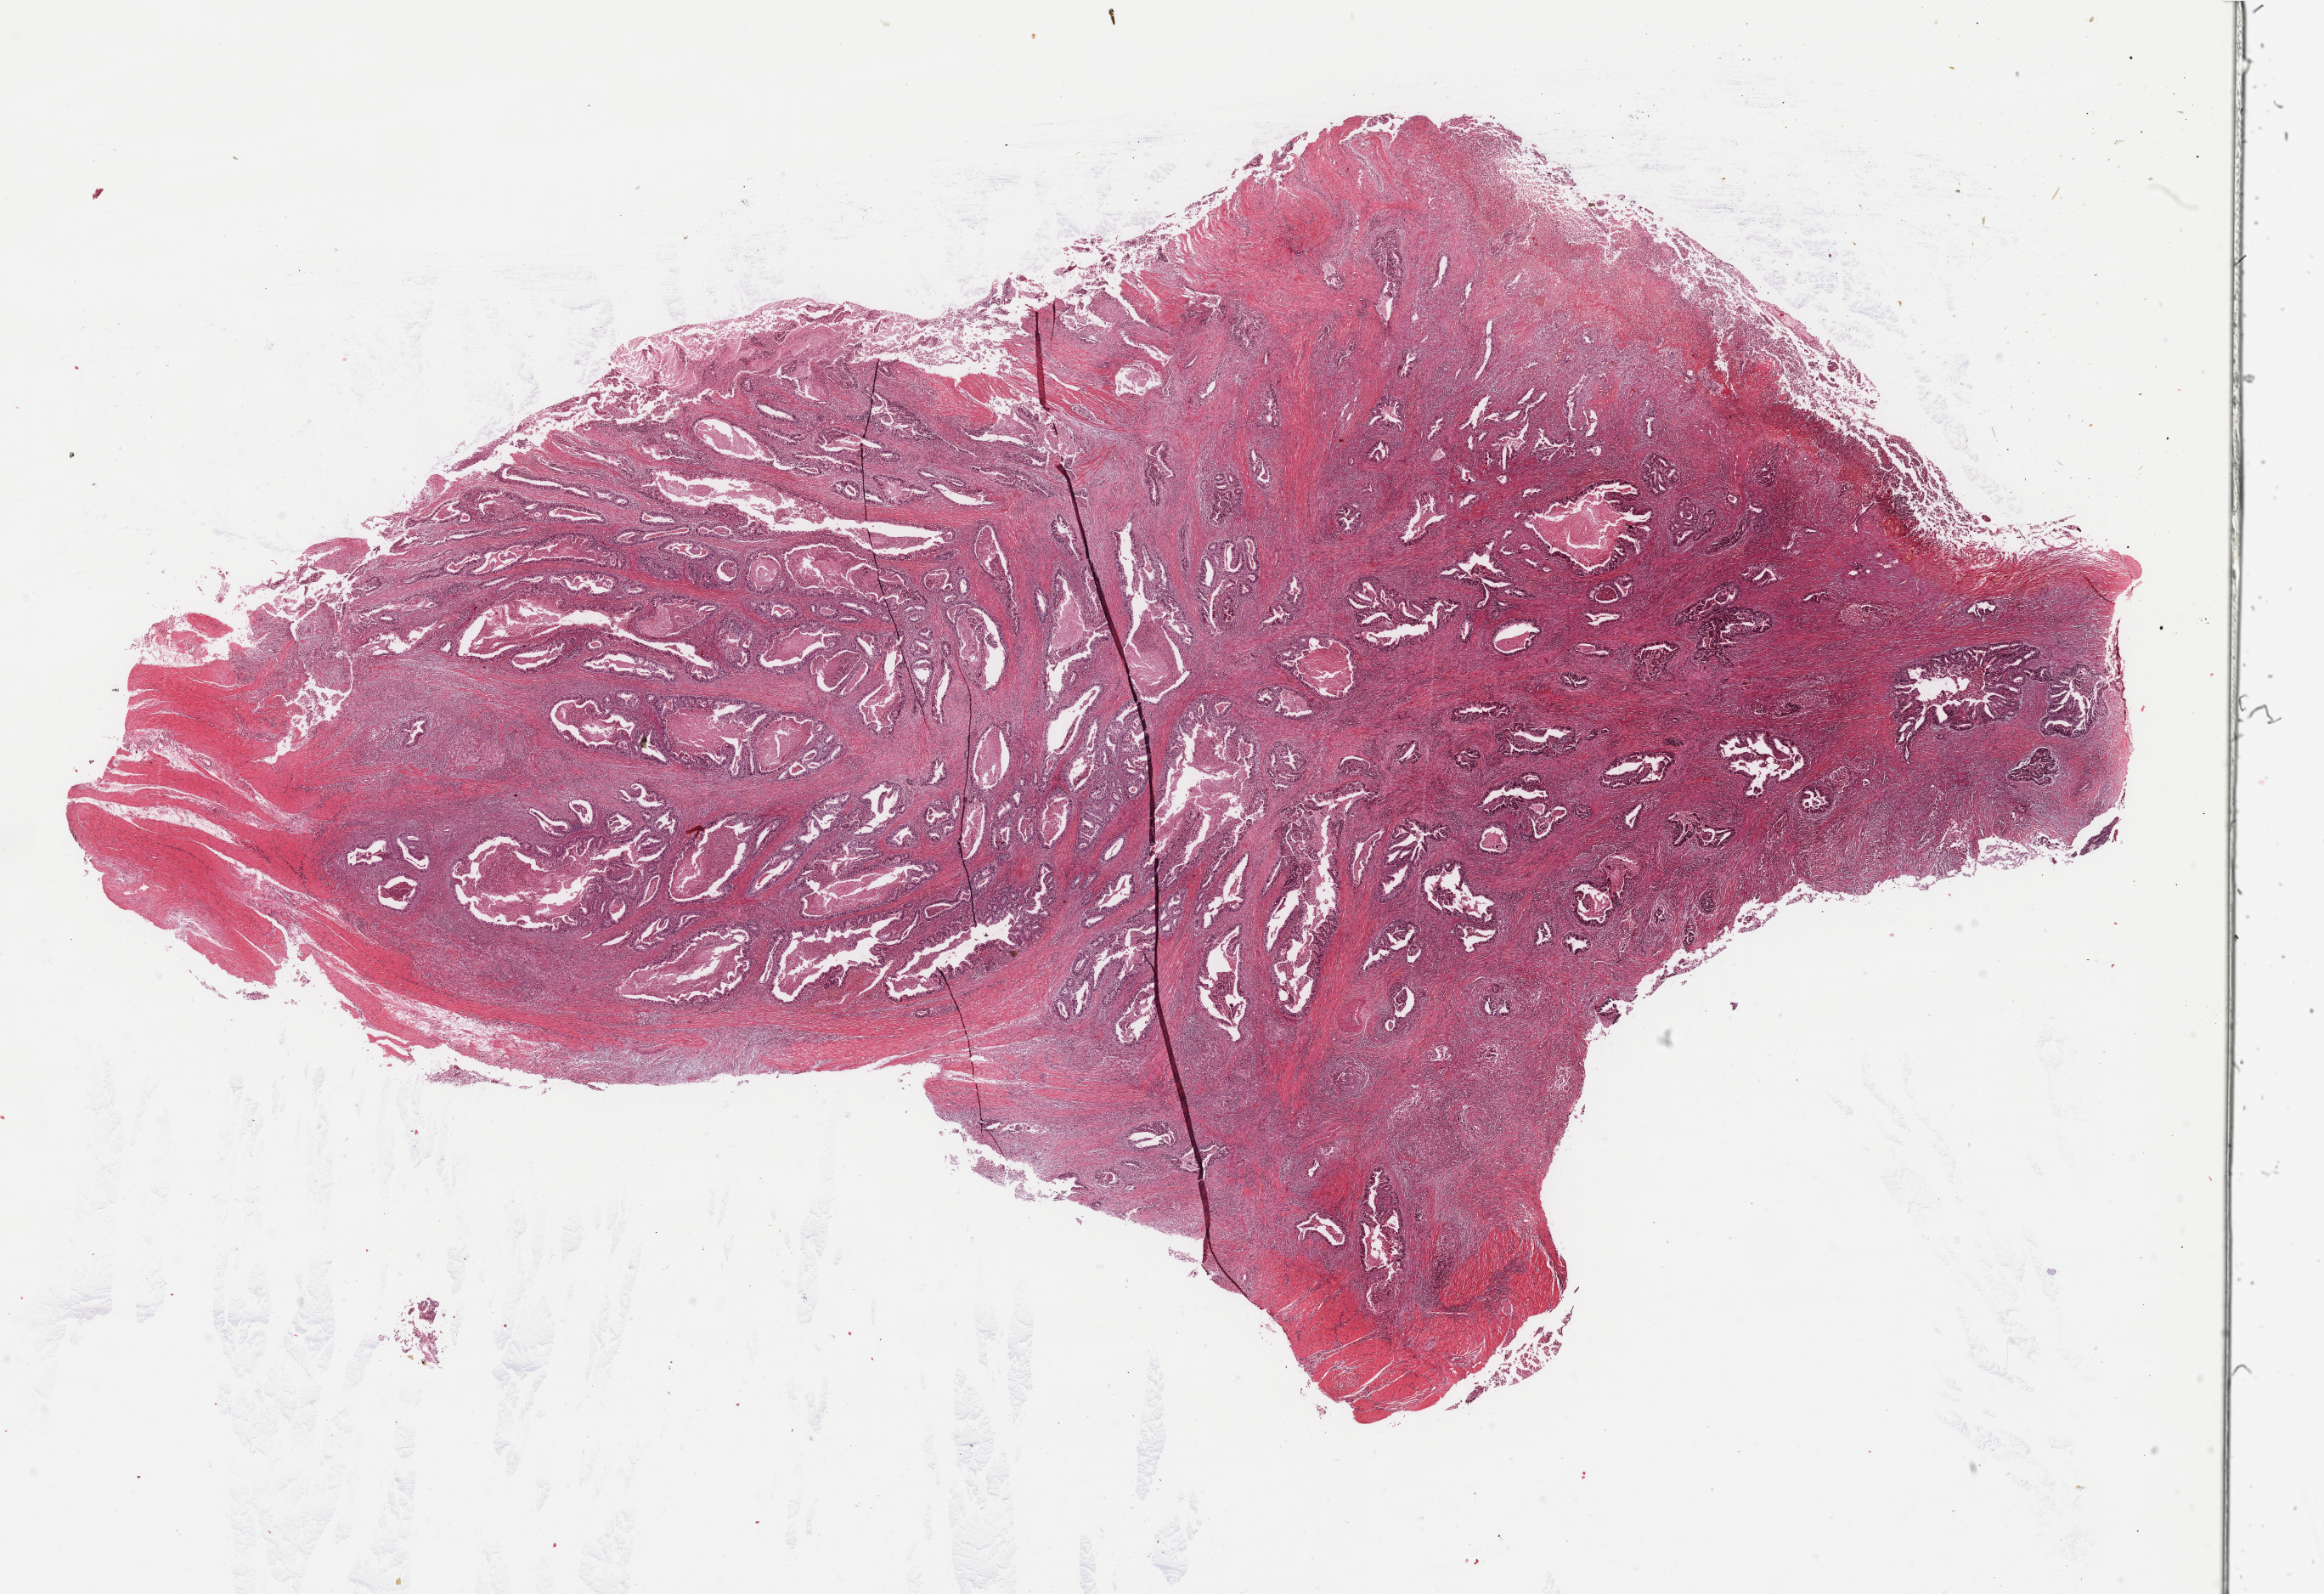
Whole-slide histology image, H&E-stained, whole scanned area (about 21.7 x 14.9 mm, slide scanned at 40x) shown as a low-resolution overview, formalin-fixed paraffin-embedded (FFPE) diagnostic section, stomach, primary tumour sample. Female patient; age at initial diagnosis 86 years. Histologic grade: G2 (moderately differentiated).
* AJCC pathologic stage: IIA (7th edition)
* histologic diagnosis: Carcinoma, diffuse type (gastric antrum)